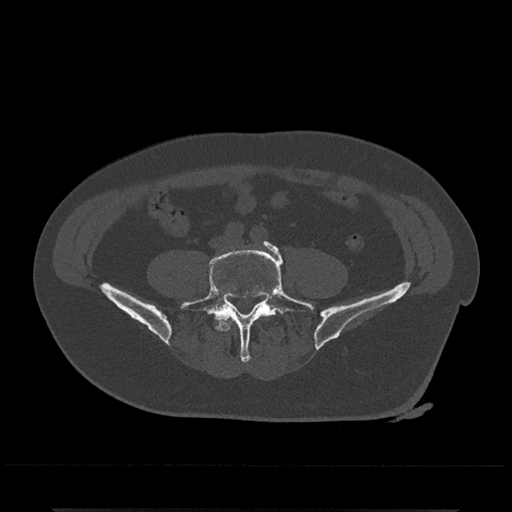
CT including the spine, one axial slice. Position 95 of 797 along the scan axis. Reconstruction kernel Br40s/3. 120 kVp. Bone window (W 1800 / L 400 HU). 0.5 mm slice thickness. 512 × 512 image matrix. Patient: male, 67 years. Case-level facts recorded for this patient, not image findings: primary cancer: prostate.
Annotated regions visible in this slice (semi-automatic segmentation, software-assisted and operator-edited):
- L4 vertebra: bounding box <220,320,232,332> (left, top, right, bottom; pixels)
- L5 vertebra: <180,241,314,363>